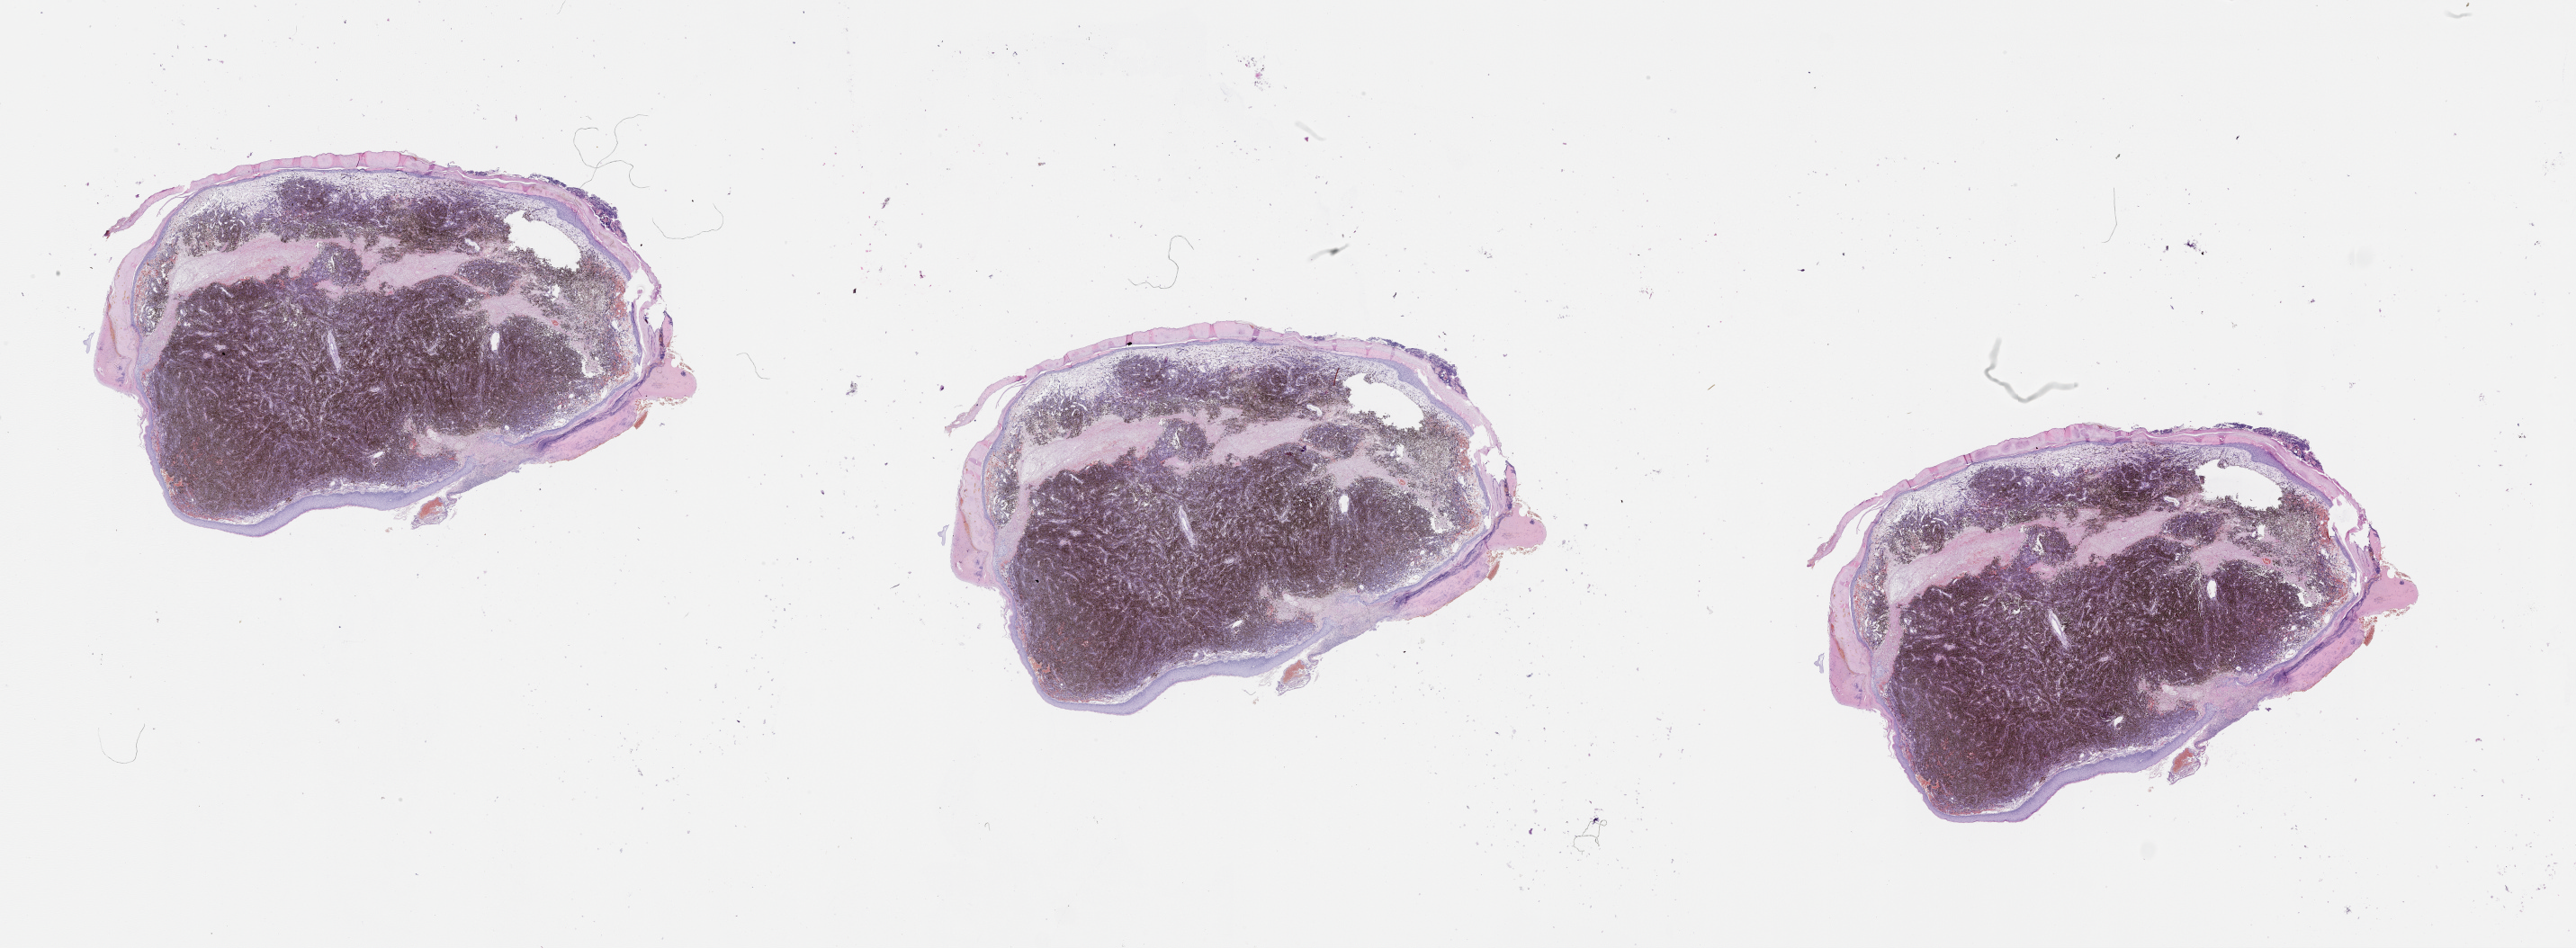
Whole-slide histology image, H&E-stained, shown as a low-resolution overview of the whole scanned area (about 46.1 x 17.0 mm, acquisition: 20x scan). Patient: male, age 82 years.
* patient diagnosis: Malignant melanoma, NOS